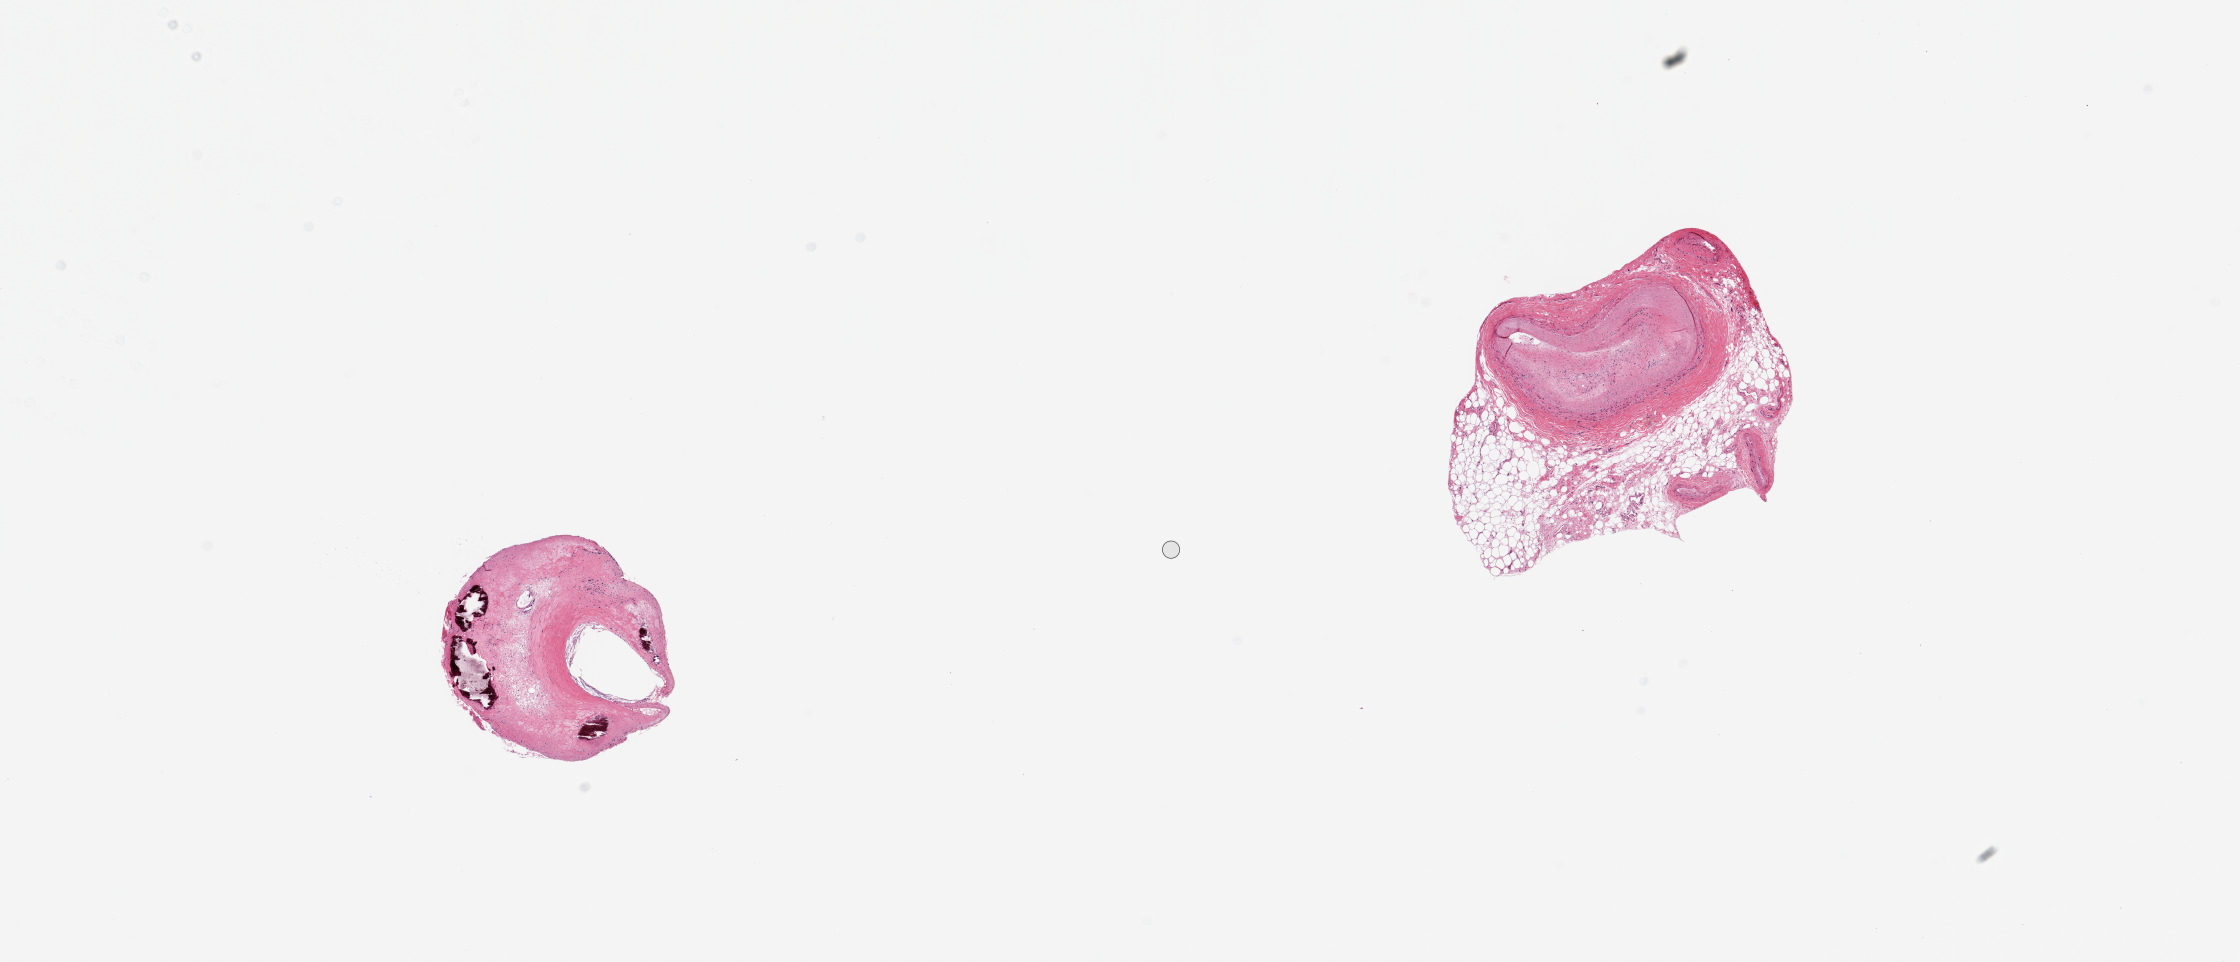
Hematoxylin and eosin (H&E) whole-slide image, shown as a low-resolution overview of the whole scanned area (about 17.7 x 7.6 mm, acquisition: 20x scan). PAXgene-fixed, paraffin-embedded tissue. Target tissue: coronary artery. Tissue donor sample. Donor: female.
Pathologist's review note for this sample: 2 pieces, 2x2 & 3x2.5mm; severe occlusive atherosclerosis in both, with calcification in one piece; other piece has 40% peripheral adipose.